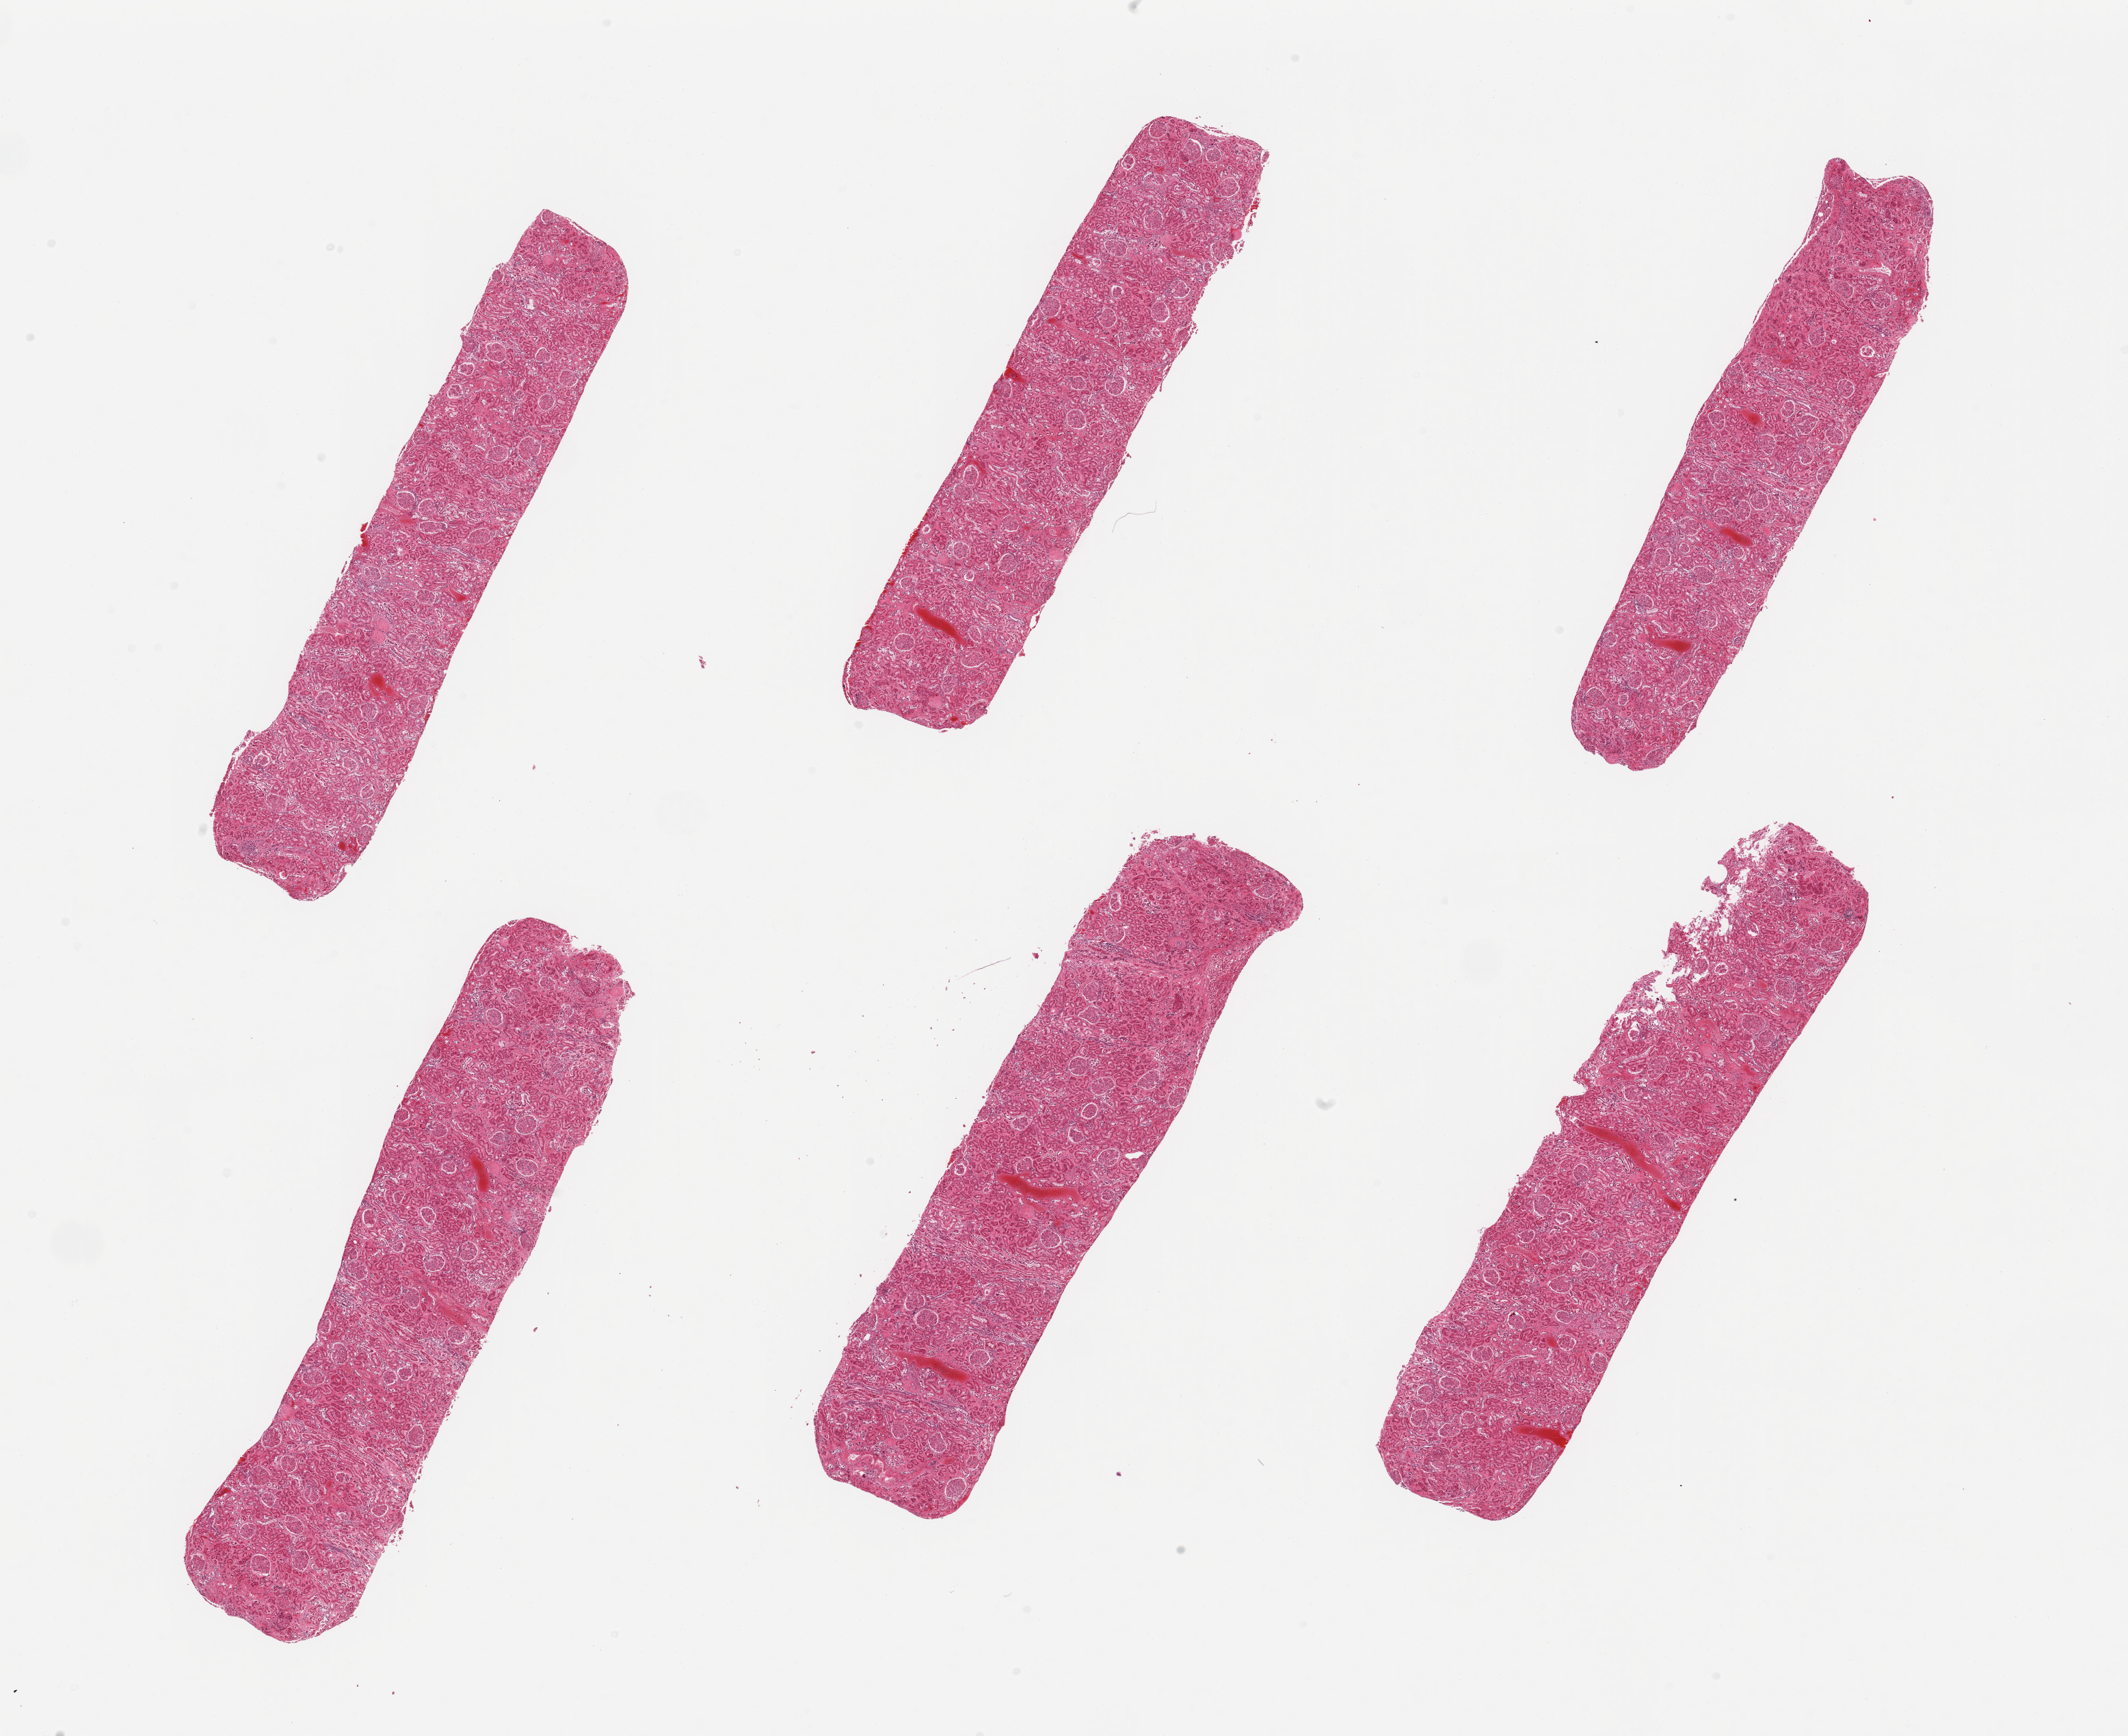
Whole-slide image, haematoxylin and eosin stain, whole scanned area (about 24.6 x 20.1 mm, slide scanned at 20x) shown as a low-resolution overview. PAXgene-fixed paraffin-embedded (PFPE) section. Sampled site (target tissue): renal cortex. Tissue donor sample. Male donor.
Review note (as recorded): 6 pieces, glomeruli present; tubules moderately autolyzed.